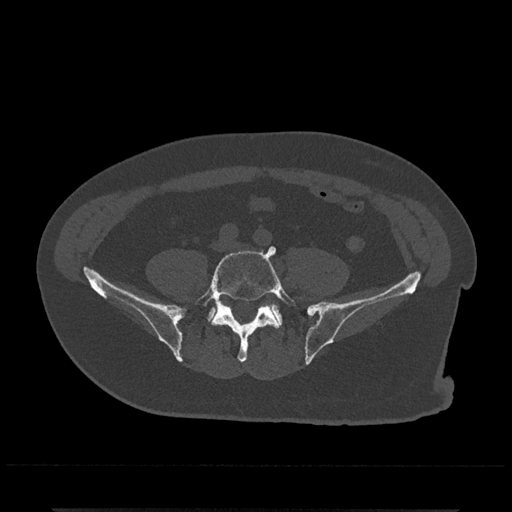
CT including the spine, one axial slice. Position 81 of 797 along the scan axis. Reconstruction kernel Br40s/3. 120 kVp. Bone window (W 1800 / L 400 HU). 512 × 512 image matrix. Male patient, age 67 years. Case-level facts recorded for this patient, not image findings: primary cancer: prostate.
Outlined on this slice (semi-automatic segmentation, software-assisted and operator-edited):
- L5 vertebra: bounding box <195,246,296,362> (left, top, right, bottom; pixels)